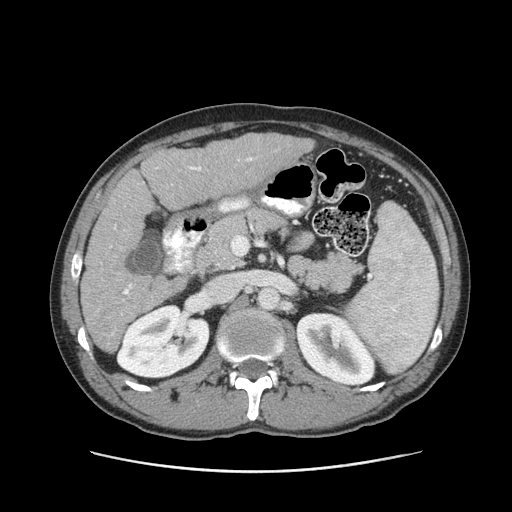
Contrast-enhanced abdominal CT (liver protocol), one axial slice. Slice 44 of 93 in the series (ordered by position). Reconstruction kernel STANDARD. 120 kVp. Soft-tissue window (W 400 / L 40 HU). 2.5 mm slice thickness. 512 × 512 image matrix, field of view 380 × 380 mm. From the clinical record (not read from this slice): diagnosis: hepatocellular carcinoma (patient treated with transarterial chemoembolisation; whether this scan precedes or follows treatment is not stated here); TNM stage (as recorded): Stage-II; Child-Pugh class: A; tumour differentiation: moderately differentiated; tumour nodularity: multinodular.
Annotated regions visible in this slice (semi-automatic segmentation, software-assisted and operator-edited):
- liver parenchyma outside the tumour (the mass and vessels are separate outlines, so this box may not span the whole liver): bounding box [x1, y1, x2, y2] px = [80, 134, 314, 352]
- liver vessels: [112, 157, 252, 334]